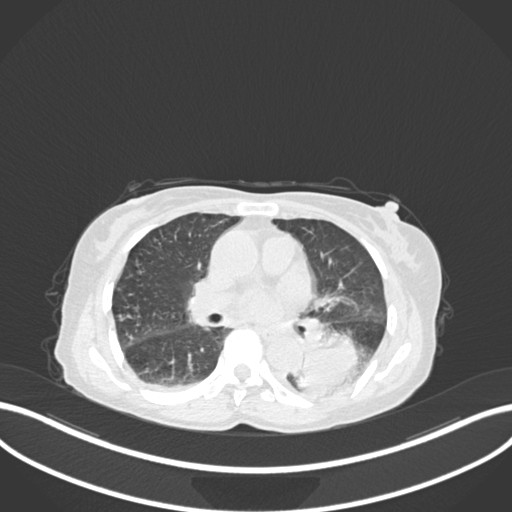
Chest CT, one axial slice; slice 89 of 233 in the series (ordered by position); reconstruction kernel B30f; lung window (W 1500 / L -600 HU); 1 mm slice thickness; 512 × 512 image matrix, field of view 400 × 400 mm. Patient: female, 78 years. Case-level facts recorded for this patient, not image findings: clinical TNM (as recorded): T3 N0 M1.
Structures marked on this image (bounding box drawn by a radiologist):
- lung tumour (recorded histology: squamous cell carcinoma): bounding box <296,335,371,396> (left, top, right, bottom; pixels)